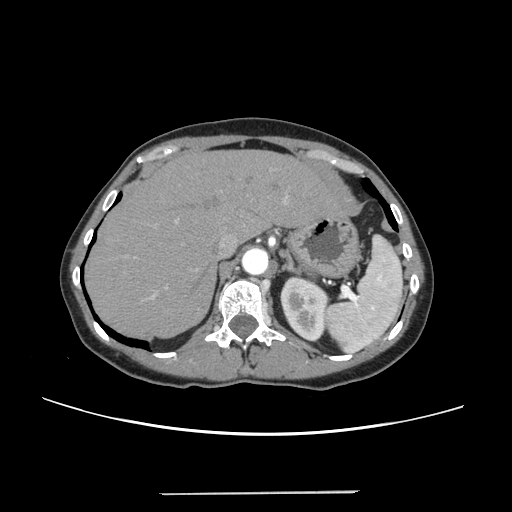
Contrast-enhanced abdominal CT, one axial slice; position 183 of 240 along the scan axis; 120 kVp; intravenous contrast given; soft-tissue window (W 400 / L 40 HU); 512 × 512 image matrix, field of view 371 × 371 mm. Female patient, age 60 years. From the clinical record (not read from this slice): diagnosis: colorectal cancer liver metastases, imaged before liver resection; multiple liver metastases: no; largest metastasis: 1.5 cm; disease in both lobes: no.
Structures marked on this image (outlined manually by an expert reader):
- hepatic veins: box from (x=219, y=235) to (x=238, y=254) px
- liver: (x=87, y=151)–(x=341, y=338)
- planned liver remnant (the part of the liver to remain after resection): (x=87, y=151)–(x=340, y=338)
- portal vein (with intrahepatic branches): (x=135, y=195)–(x=289, y=298)